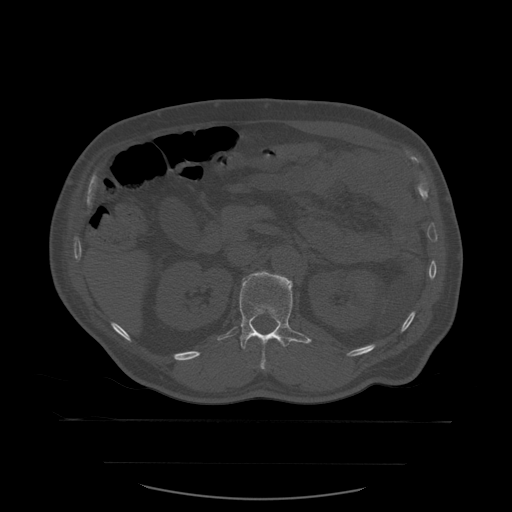
CT including the spine, one axial slice; slice 248 of 590 in the series (ordered by position); bone window (W 1800 / L 400 HU); 512 × 512 image matrix, field of view 479 × 479 mm. Patient age 71 years. From the clinical record (not read from this slice): primary cancer: lung; vertebrae with lytic lesions (as recorded): T1, T2, L5, S1.
Structures marked on this image (semi-automatically segmented with operator editing):
- L1 vertebra: bounding box <217,271,312,370> (left, top, right, bottom; pixels)
- T12 vertebra: <278,340,285,347>